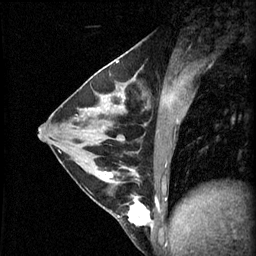
Breast MRI (dynamic contrast-enhanced), one sagittal slice; 3 images stored at this slice position (order not interpretable as contrast timing); 1.5 T; TE 4.2 ms, TR 11 ms; 256 × 256 image matrix. Female patient, age 29 years.
Annotated regions visible in this slice (semi-automatic segmentation, software-assisted and operator-edited):
- analysis volume of interest (the breast-tissue region the enhancement analysis was run in; not a lesion): bounding box <93,164,153,229> (left, top, right, bottom; pixels)
- tumour enhancement mask (voxels above the 70 % enhancement threshold inside the analysis volume of interest): <104,168,153,227>